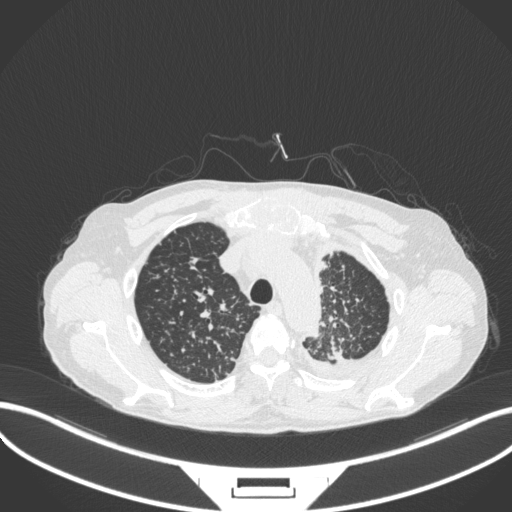
Chest CT, one axial slice; position 280 of 319 along the scan axis; 120 kVp; lung window (W 1500 / L -600 HU); 1 mm slice thickness; 512 × 512 image matrix. Patient: male, 58 years. Case-level facts recorded for this patient, not image findings: clinical TNM (as recorded): T1c N3 M1.
Structures marked on this image (rectangle marked by the reading radiologist):
- lung tumour (recorded histology: adenocarcinoma): bounding box (x1, y1, x2, y2) in pixels: (324, 336, 344, 361)